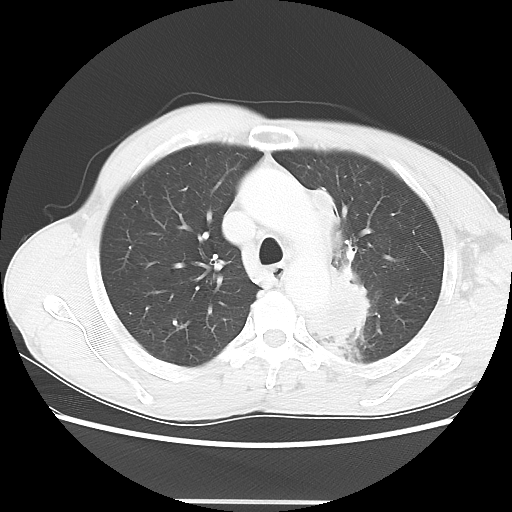
Chest CT, one axial slice; slice 47 of 62 in the series (ordered by position); reconstruction kernel LUNG; lung window (W 1500 / L -600 HU); 5 mm slice thickness; 512 × 512 image matrix, field of view 360 × 360 mm. Patient: male, 61 years. From the clinical record (not read from this slice): clinical TNM (as recorded): T3 N1 M1.
Annotated regions visible in this slice (rectangle marked by the reading radiologist):
- lung tumour (recorded histology: adenocarcinoma): bounding box (x1, y1, x2, y2) in pixels: (305, 182, 378, 347)